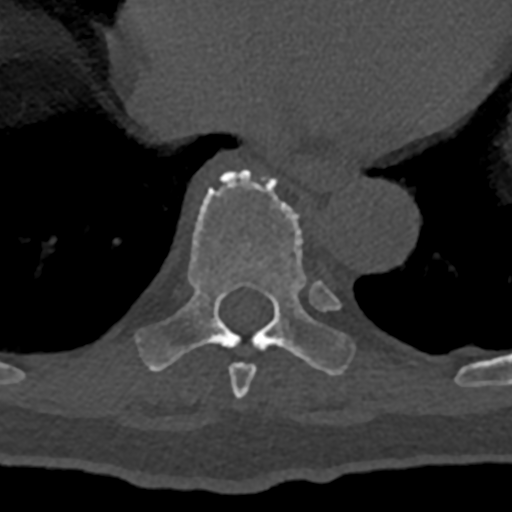
CT including the spine, one axial slice. Slice 666 of 797 in the series (ordered by position). Reconstruction kernel Br40s/3. 120 kVp. Bone window (W 1800 / L 400 HU). 512 × 512 image matrix. Male patient, age 74 years. From the clinical record (not read from this slice): primary cancer: renal; vertebrae with lytic lesions (as recorded): T10, L1, L2, L3, L4, L5.
Structures marked on this image (semi-automatic segmentation, software-assisted and operator-edited):
- T8 vertebra: bounding box (x1, y1, x2, y2) in pixels: (229, 363, 256, 399)
- T9 vertebra: (135, 170, 354, 376)